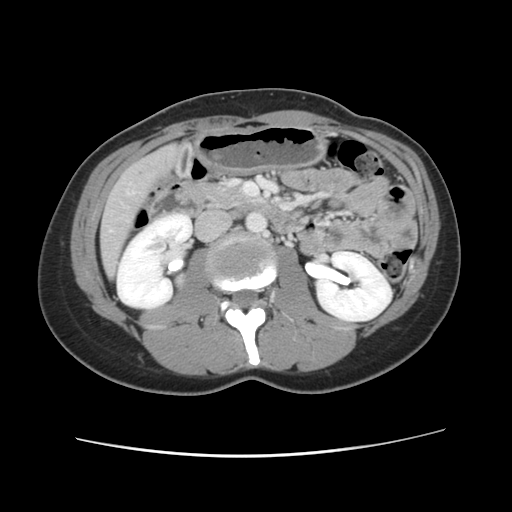
Contrast-enhanced abdominal CT, one axial slice; slice 30 of 134 in the series (ordered by position); 120 kVp; intravenous contrast given; soft-tissue window (W 400 / L 40 HU); 2.5 mm slice thickness; 512 × 512 image matrix, field of view 339 × 339 mm. Female patient, age 33 years. Case-level facts recorded for this patient, not image findings: diagnosis: colorectal cancer liver metastases, imaged before liver resection; multiple liver metastases: yes; largest metastasis: 4.5 cm; disease in both lobes: yes.
Structures marked on this image (outlined manually by an expert reader):
- liver: box from (x=101, y=145) to (x=183, y=279) px
- planned liver remnant (the part of the liver to remain after resection): (x=101, y=243)–(x=118, y=278)